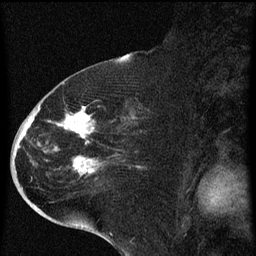
Breast MRI (dynamic contrast-enhanced), one sagittal slice. Slice 31 of 60 in the series (ordered by position). Dynamic contrast-enhanced series, image 2 of 4 at this slice position (ordered by acquisition). 1.5 T. TE 4.2 ms, TR 8 ms. 2 mm slice thickness. 256 × 256 image matrix, field of view 180 × 180 mm. Female patient, age 71 years.
Outlined on this slice (semi-automatic segmentation, software-assisted and operator-edited):
- analysis volume of interest (the breast-tissue region the enhancement analysis was run in; not a lesion): bounding box (x1, y1, x2, y2) in pixels: (32, 86, 141, 205)
- tumour enhancement mask (voxels above the 70 % enhancement threshold inside the analysis volume of interest): (38, 108, 98, 173)